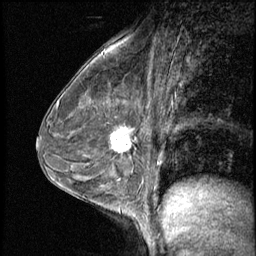
Breast MRI (dynamic contrast-enhanced), one sagittal slice; position 36 of 56 along the scan axis; 3 images stored at this slice position (order not interpretable as contrast timing); 1.5 T; TE 4.2 ms, TR 8.7 ms; 2.5 mm slice thickness; 256 × 256 image matrix, field of view 180 × 180 mm. Patient: female, 43 years. From the clinical record (not read from this slice): setting: breast cancer imaged before/during neoadjuvant chemotherapy; receptor status: HR-positive, HER2-negative.
Outlined on this slice (semi-automatically segmented with operator editing):
- analysis volume of interest (the breast-tissue region the enhancement analysis was run in; not a lesion): bounding box [x1, y1, x2, y2] px = [101, 120, 145, 165]
- tumour enhancement mask (voxels above the 140 % enhancement threshold inside the analysis volume of interest): [111, 128, 131, 153]